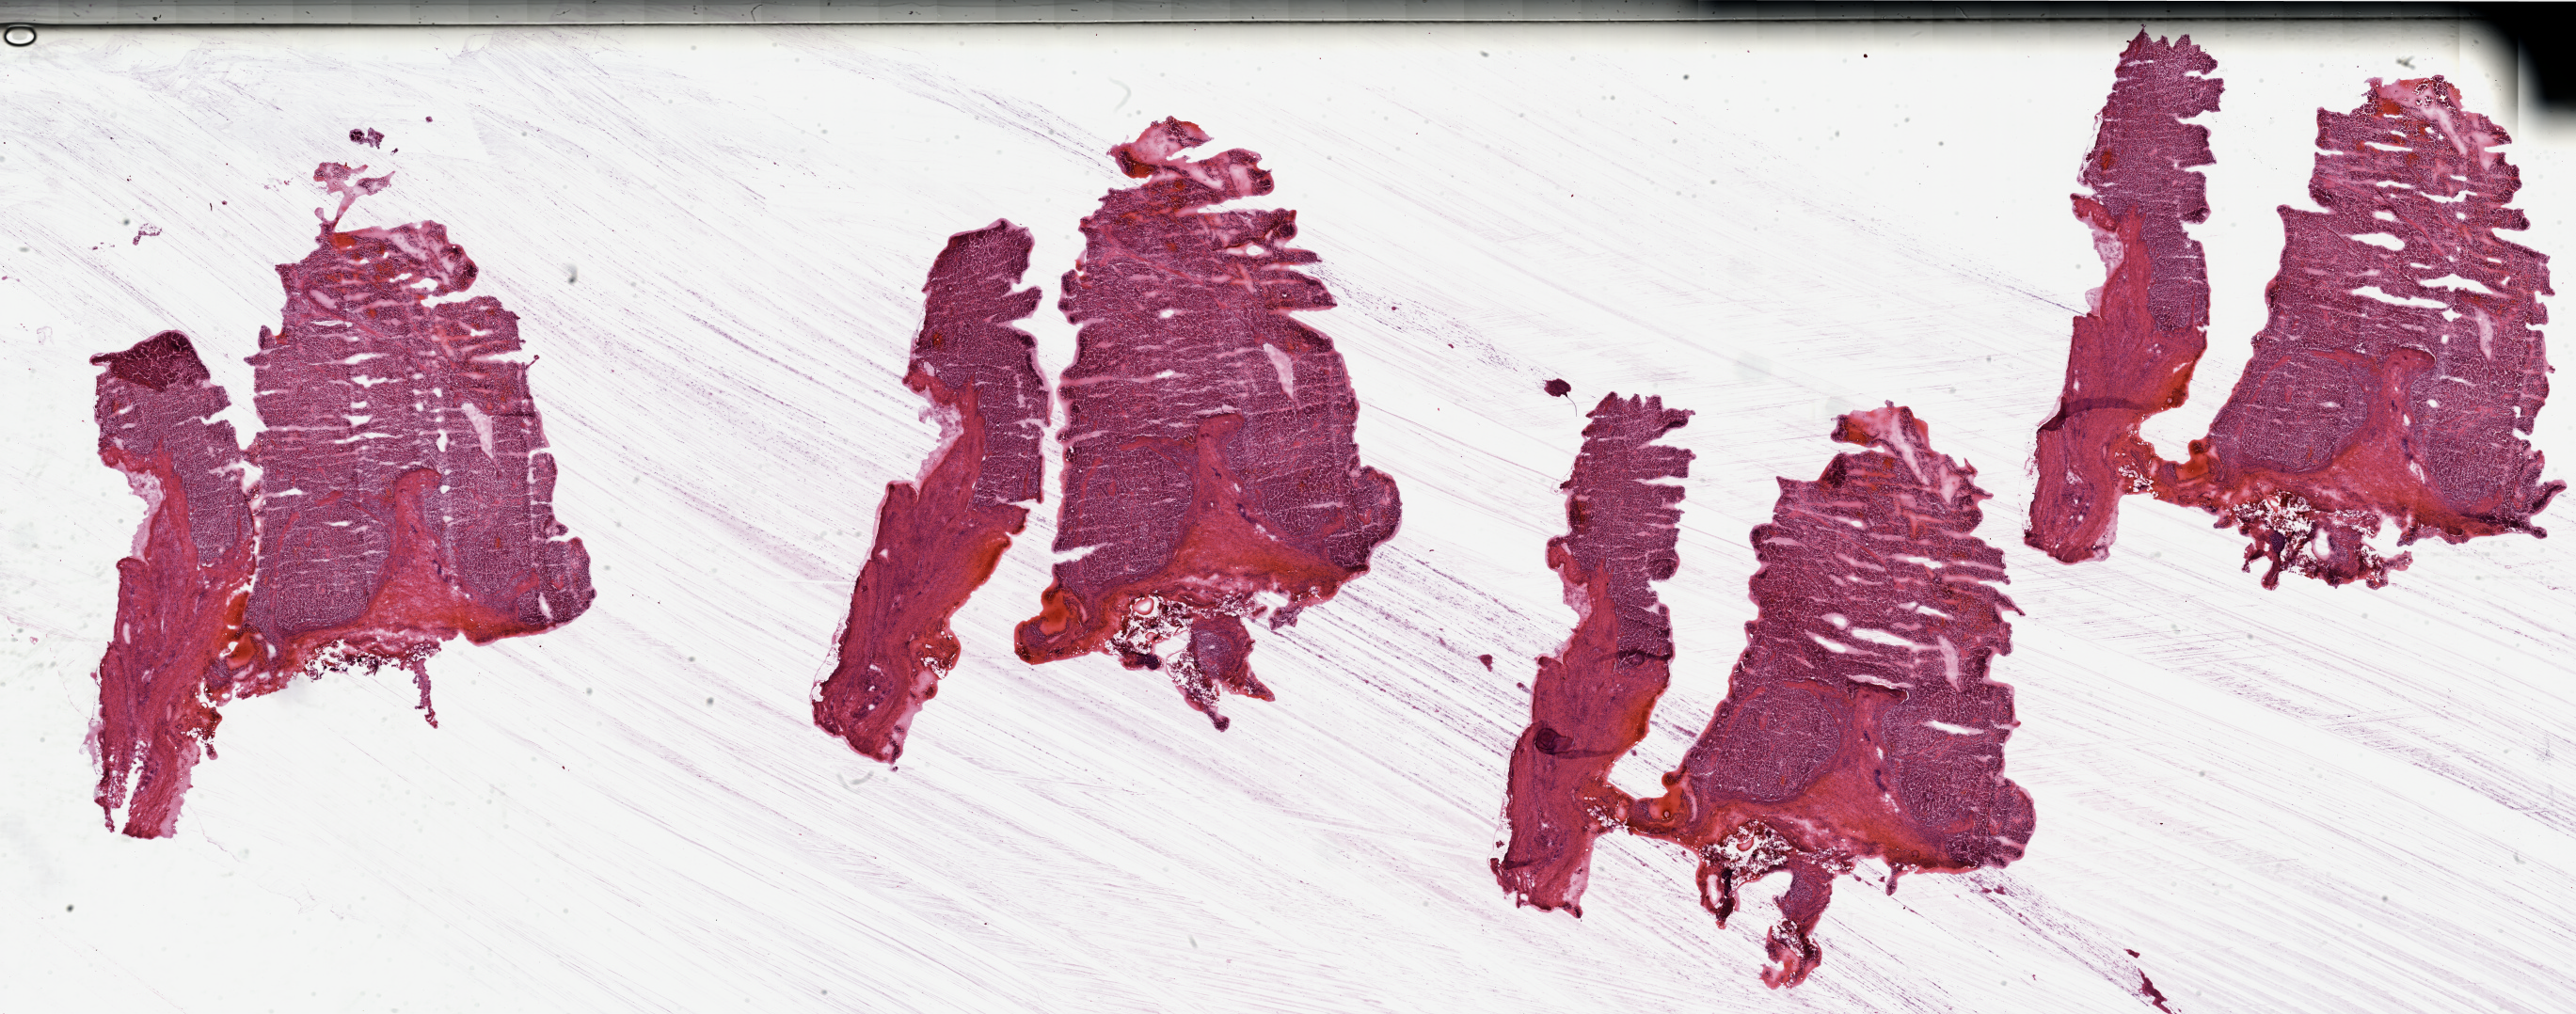
H&E whole-slide image, whole scanned area (about 43.3 x 17.1 mm, from a 20x scan) shown as a low-resolution overview; kidney, tumour tissue. 60-year-old female patient. Histologic grade: G1 (well differentiated).
• AJCC pathologic stage: I
• histologic diagnosis: Renal cell carcinoma, NOS
• primary tumour site (as recorded): middle